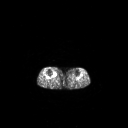
FDG PET of an extremity soft-tissue mass (from a PET/CT study), one axial slice; 3.27 mm slice thickness; 128 × 128 image matrix, field of view 700 × 700 mm. Female patient, age 65 years. Case-level facts recorded for this patient, not image findings: histological type: undifferentiated – high grade; grade: high; site of the primary tumour: right thigh.
Structures marked on this image (expert contour drawn on MRI and transferred to this co-registered scan by the dataset authors):
- gross tumour volume (mass): bounding box [x1, y1, x2, y2] px = [53, 72, 57, 77]